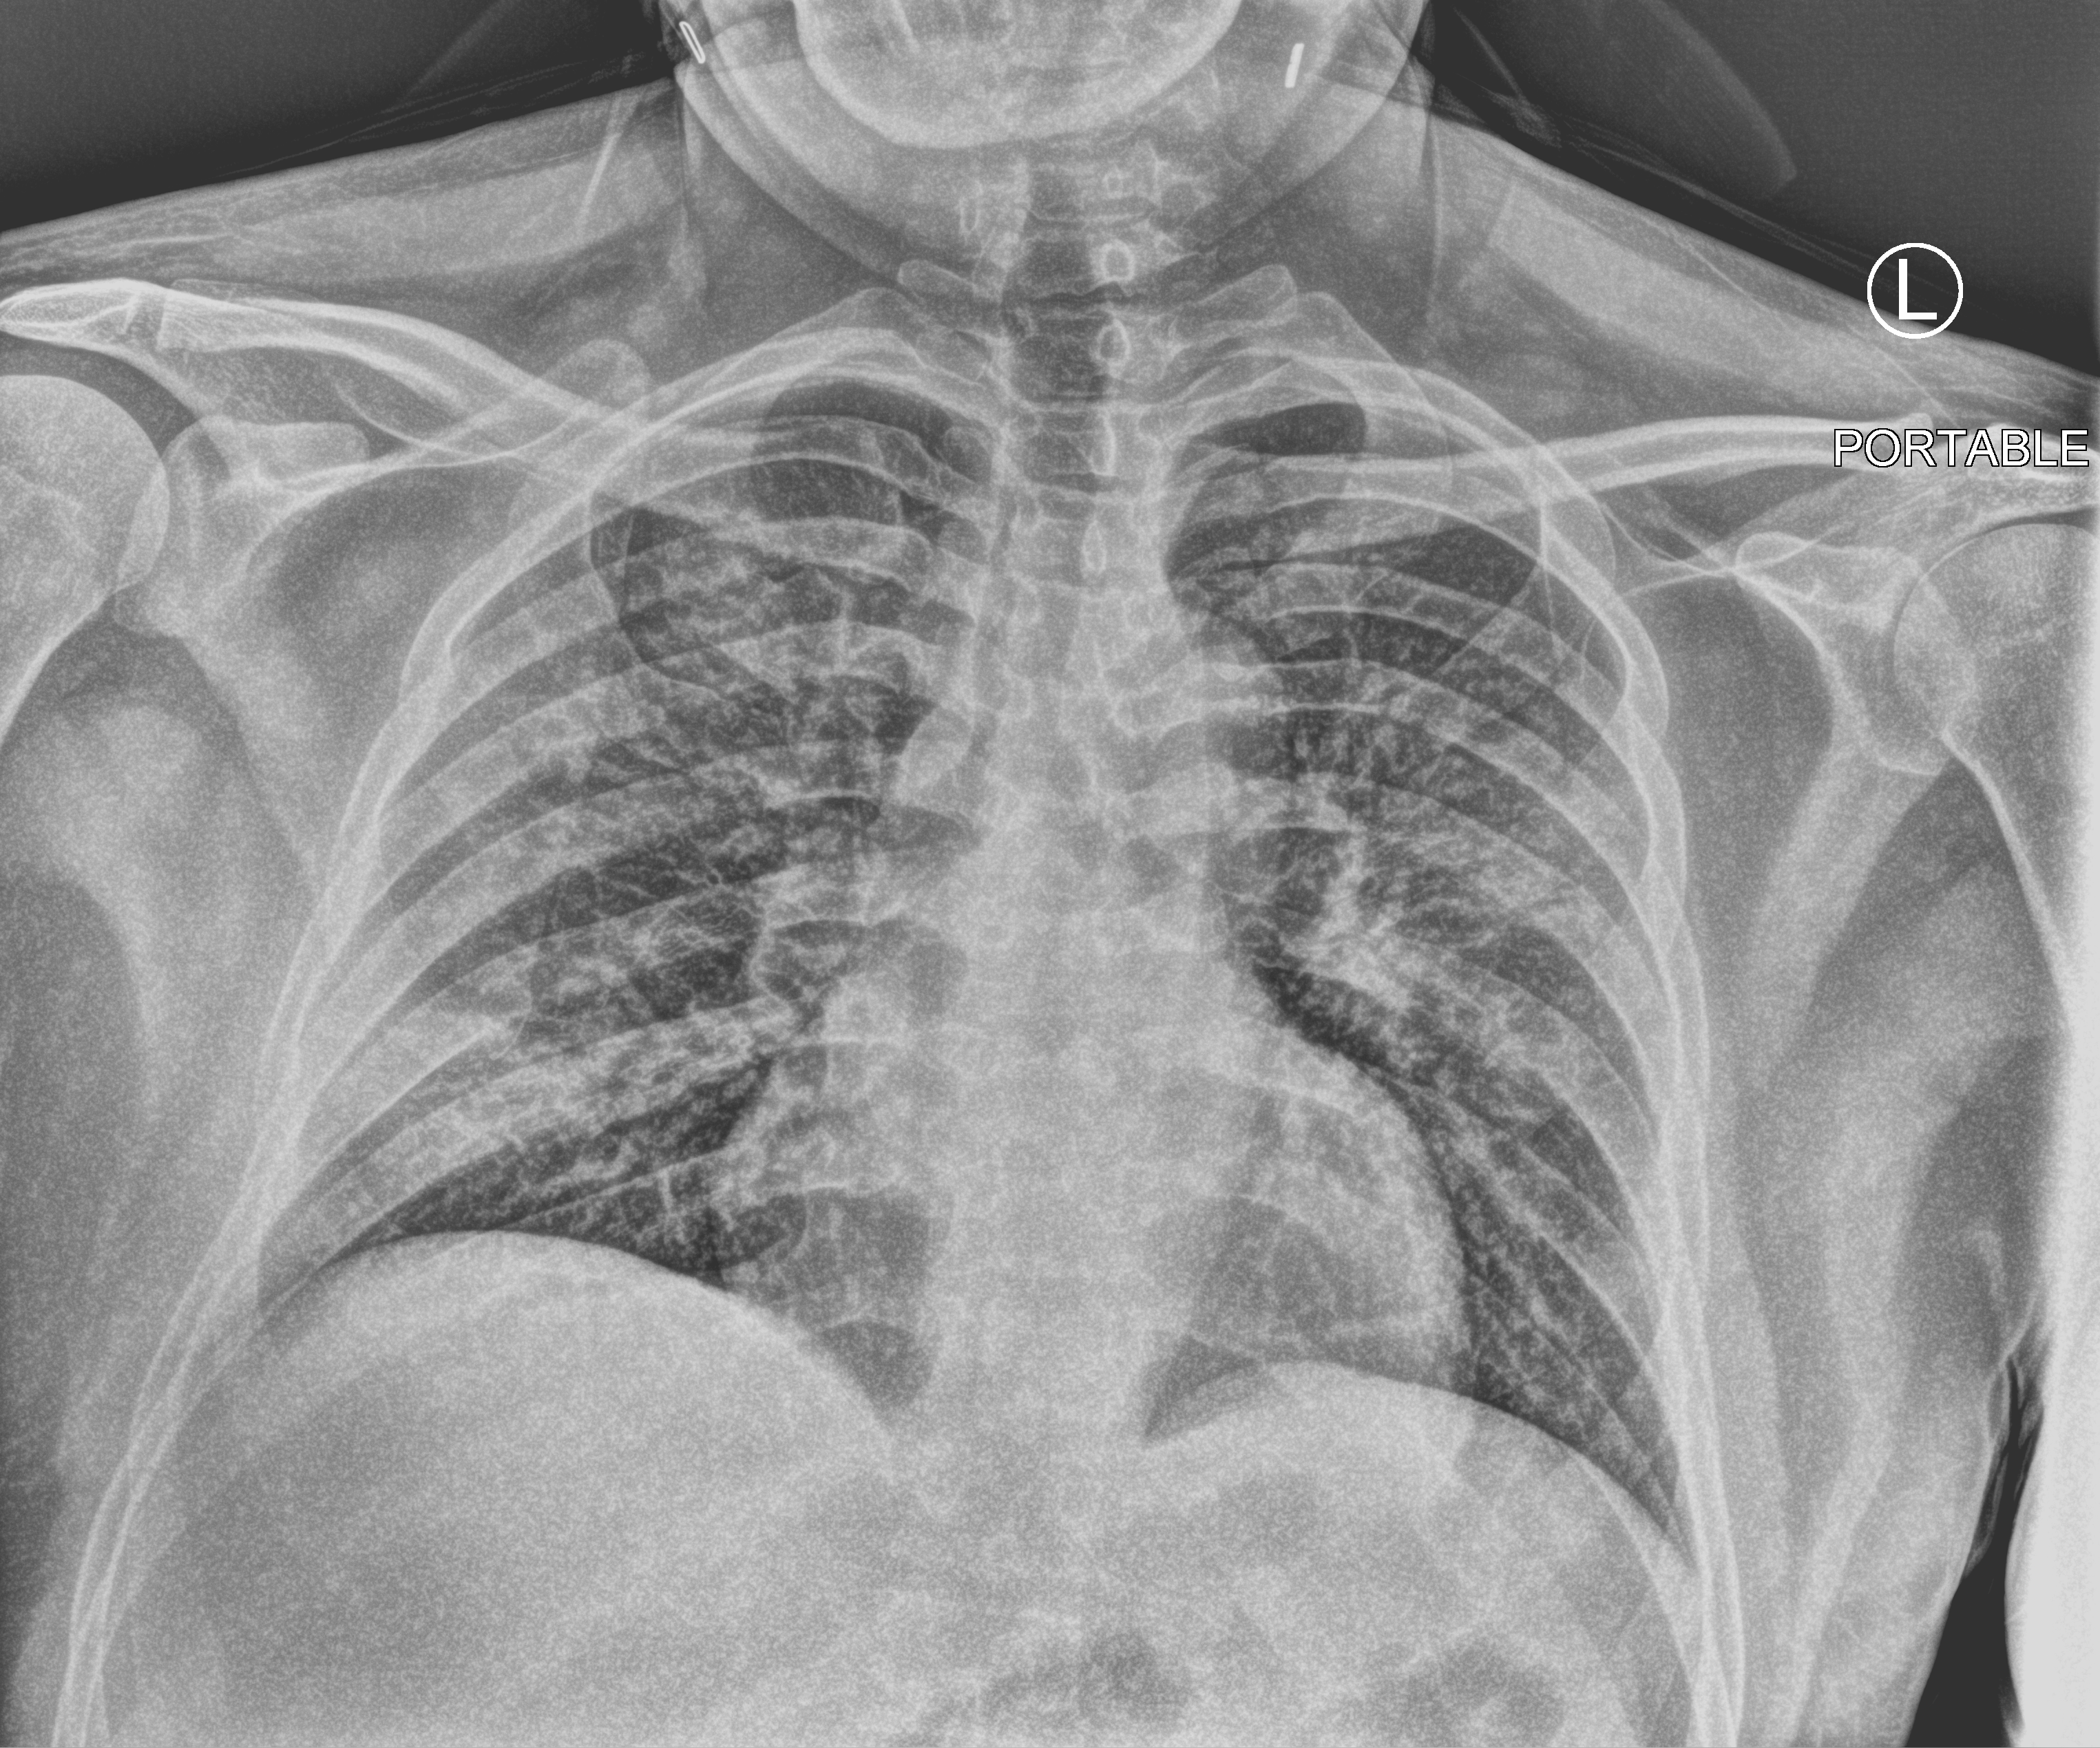
Portable chest radiograph; anteroposterior (AP) projection. Male patient hospitalised with COVID-19, age 18–59 years.
Admission-level facts for this patient (not findings on this image; timing relative to this image not recorded):
- length of hospital stay: 1 day